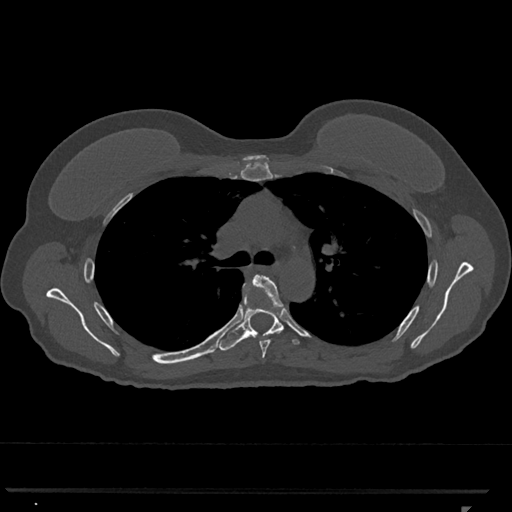
CT including the spine, one axial slice; position 783 of 793 along the scan axis; reconstruction kernel Br40s/3; bone window (W 1800 / L 400 HU); 512 × 512 image matrix, field of view 380 × 380 mm. Patient: female, 62 years. From the clinical record (not read from this slice): primary cancer: renal.
Outlined on this slice (semi-automatically segmented with operator editing):
- T5 vertebra: bounding box (x1, y1, x2, y2) in pixels: (253, 274, 283, 359)
- T6 vertebra: (219, 281, 300, 351)